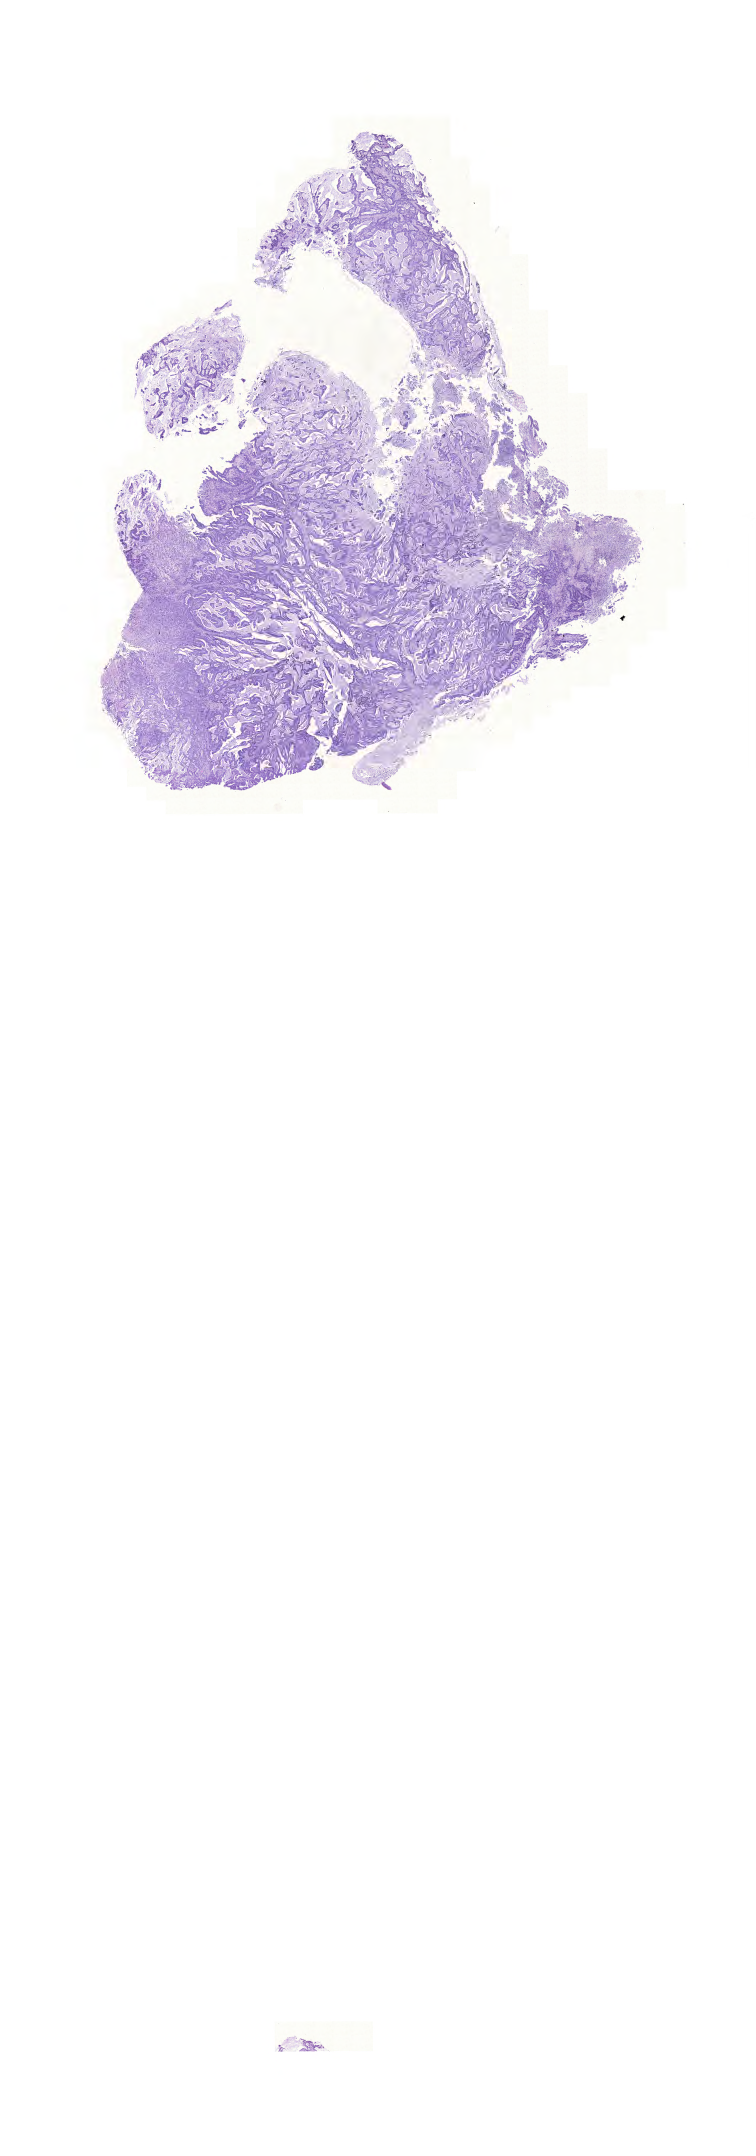
Digitized H&E tissue section (whole slide) — a low-resolution overview of the entire scanned area, about 11.2 x 32.1 mm (slide scanned at 20x). Formalin-fixed paraffin-embedded (FFPE) diagnostic section. Colon, primary tumour sample. Female, age 74 years at initial diagnosis.
AJCC pathologic stage: III (5th edition). Pathologic diagnosis: Mucinous adenocarcinoma. Lymph nodes positive (case pathology): 7 of 26 examined.